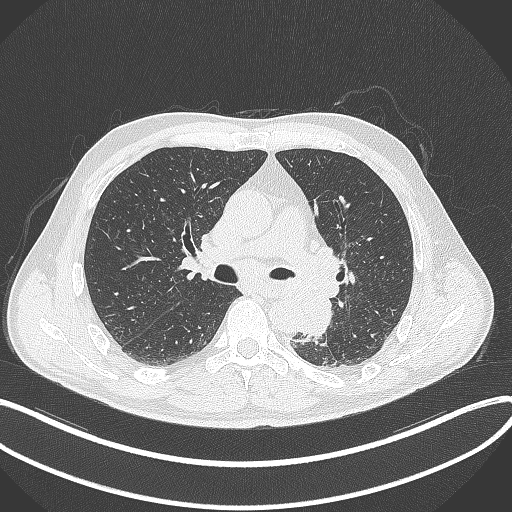
Chest CT, one axial slice. Position 206 of 329 along the scan axis. 120 kVp. Lung window (W 1500 / L -600 HU). 1 mm slice thickness. 512 × 512 image matrix, field of view 400 × 400 mm. Patient: male, 59 years. From the clinical record (not read from this slice): clinical TNM (as recorded): T2a N2 M0.
Annotated regions visible in this slice (rectangle marked by the reading radiologist):
- lung tumour (recorded histology: squamous cell carcinoma): bounding box (x1, y1, x2, y2) in pixels: (296, 293, 337, 341)